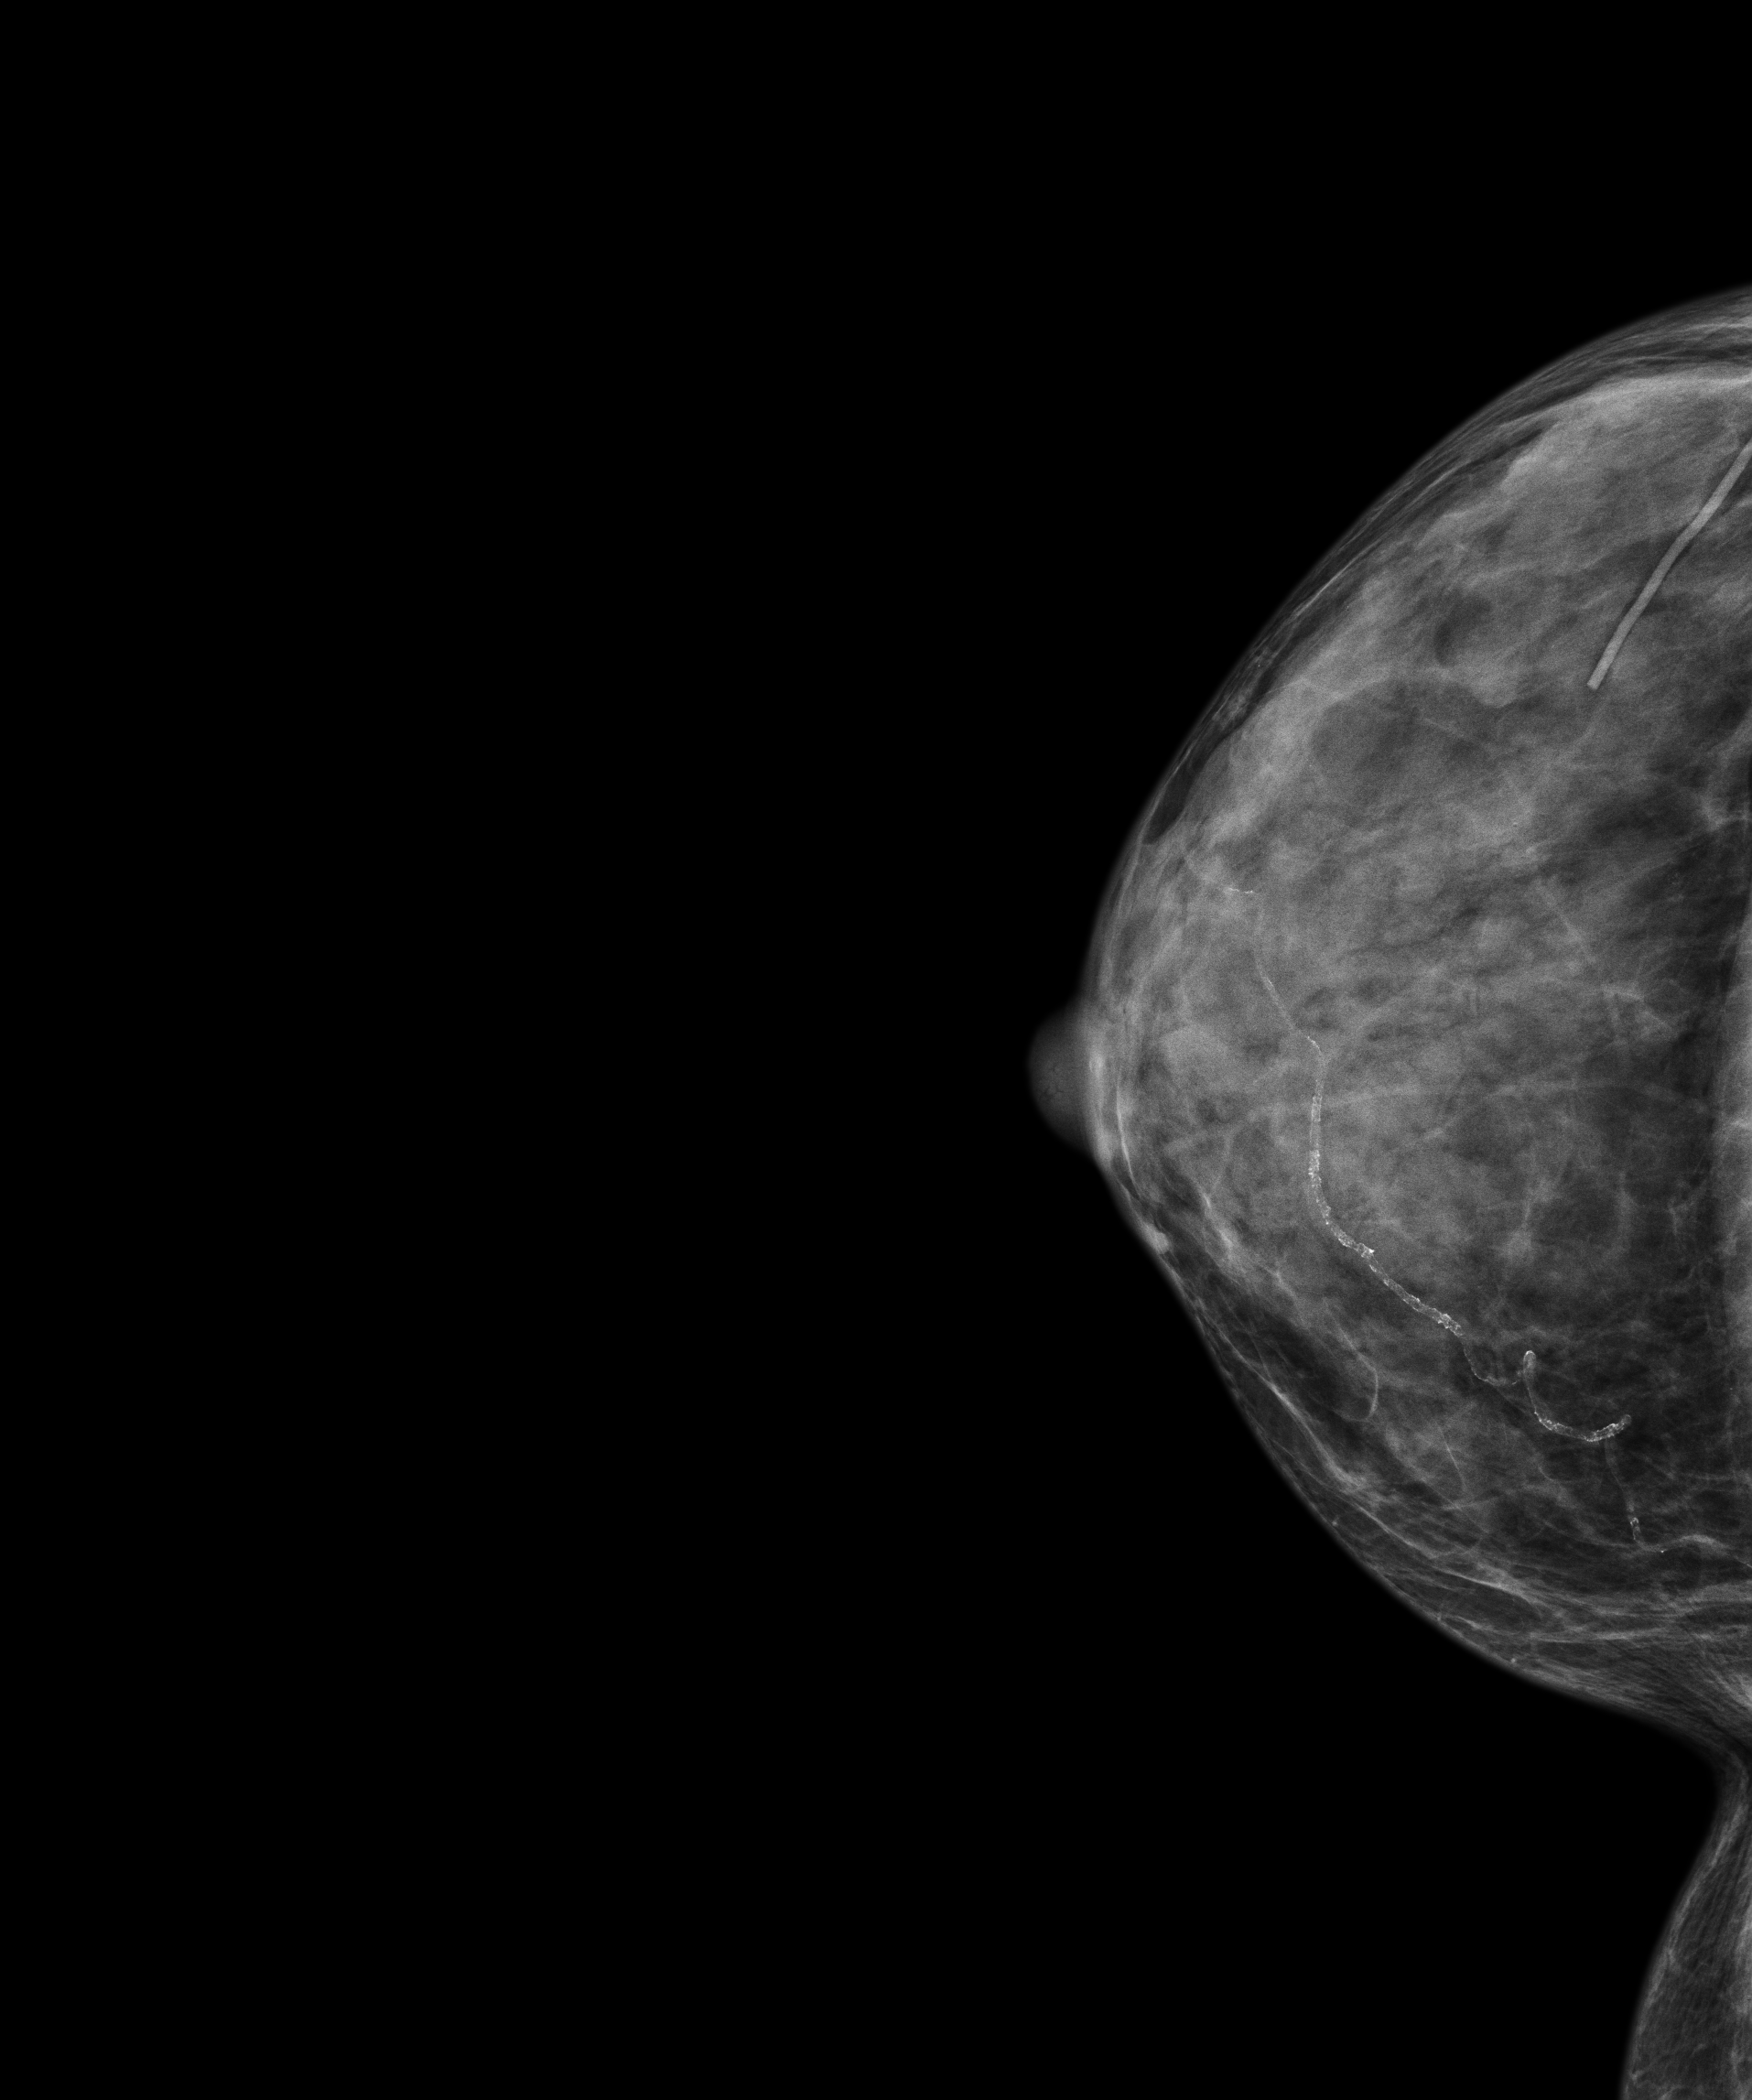
Full-field digital mammogram (FFDM); right breast; craniocaudal (CC) view; screening examination. Patient: female, 59 years.
BI-RADS breast density category at the screening exam (both breasts, scale 1–4): 4. Final BI-RADS assessment for this screening round (tomosynthesis exam, both breasts): category 1. Recall: no recall after this screen.